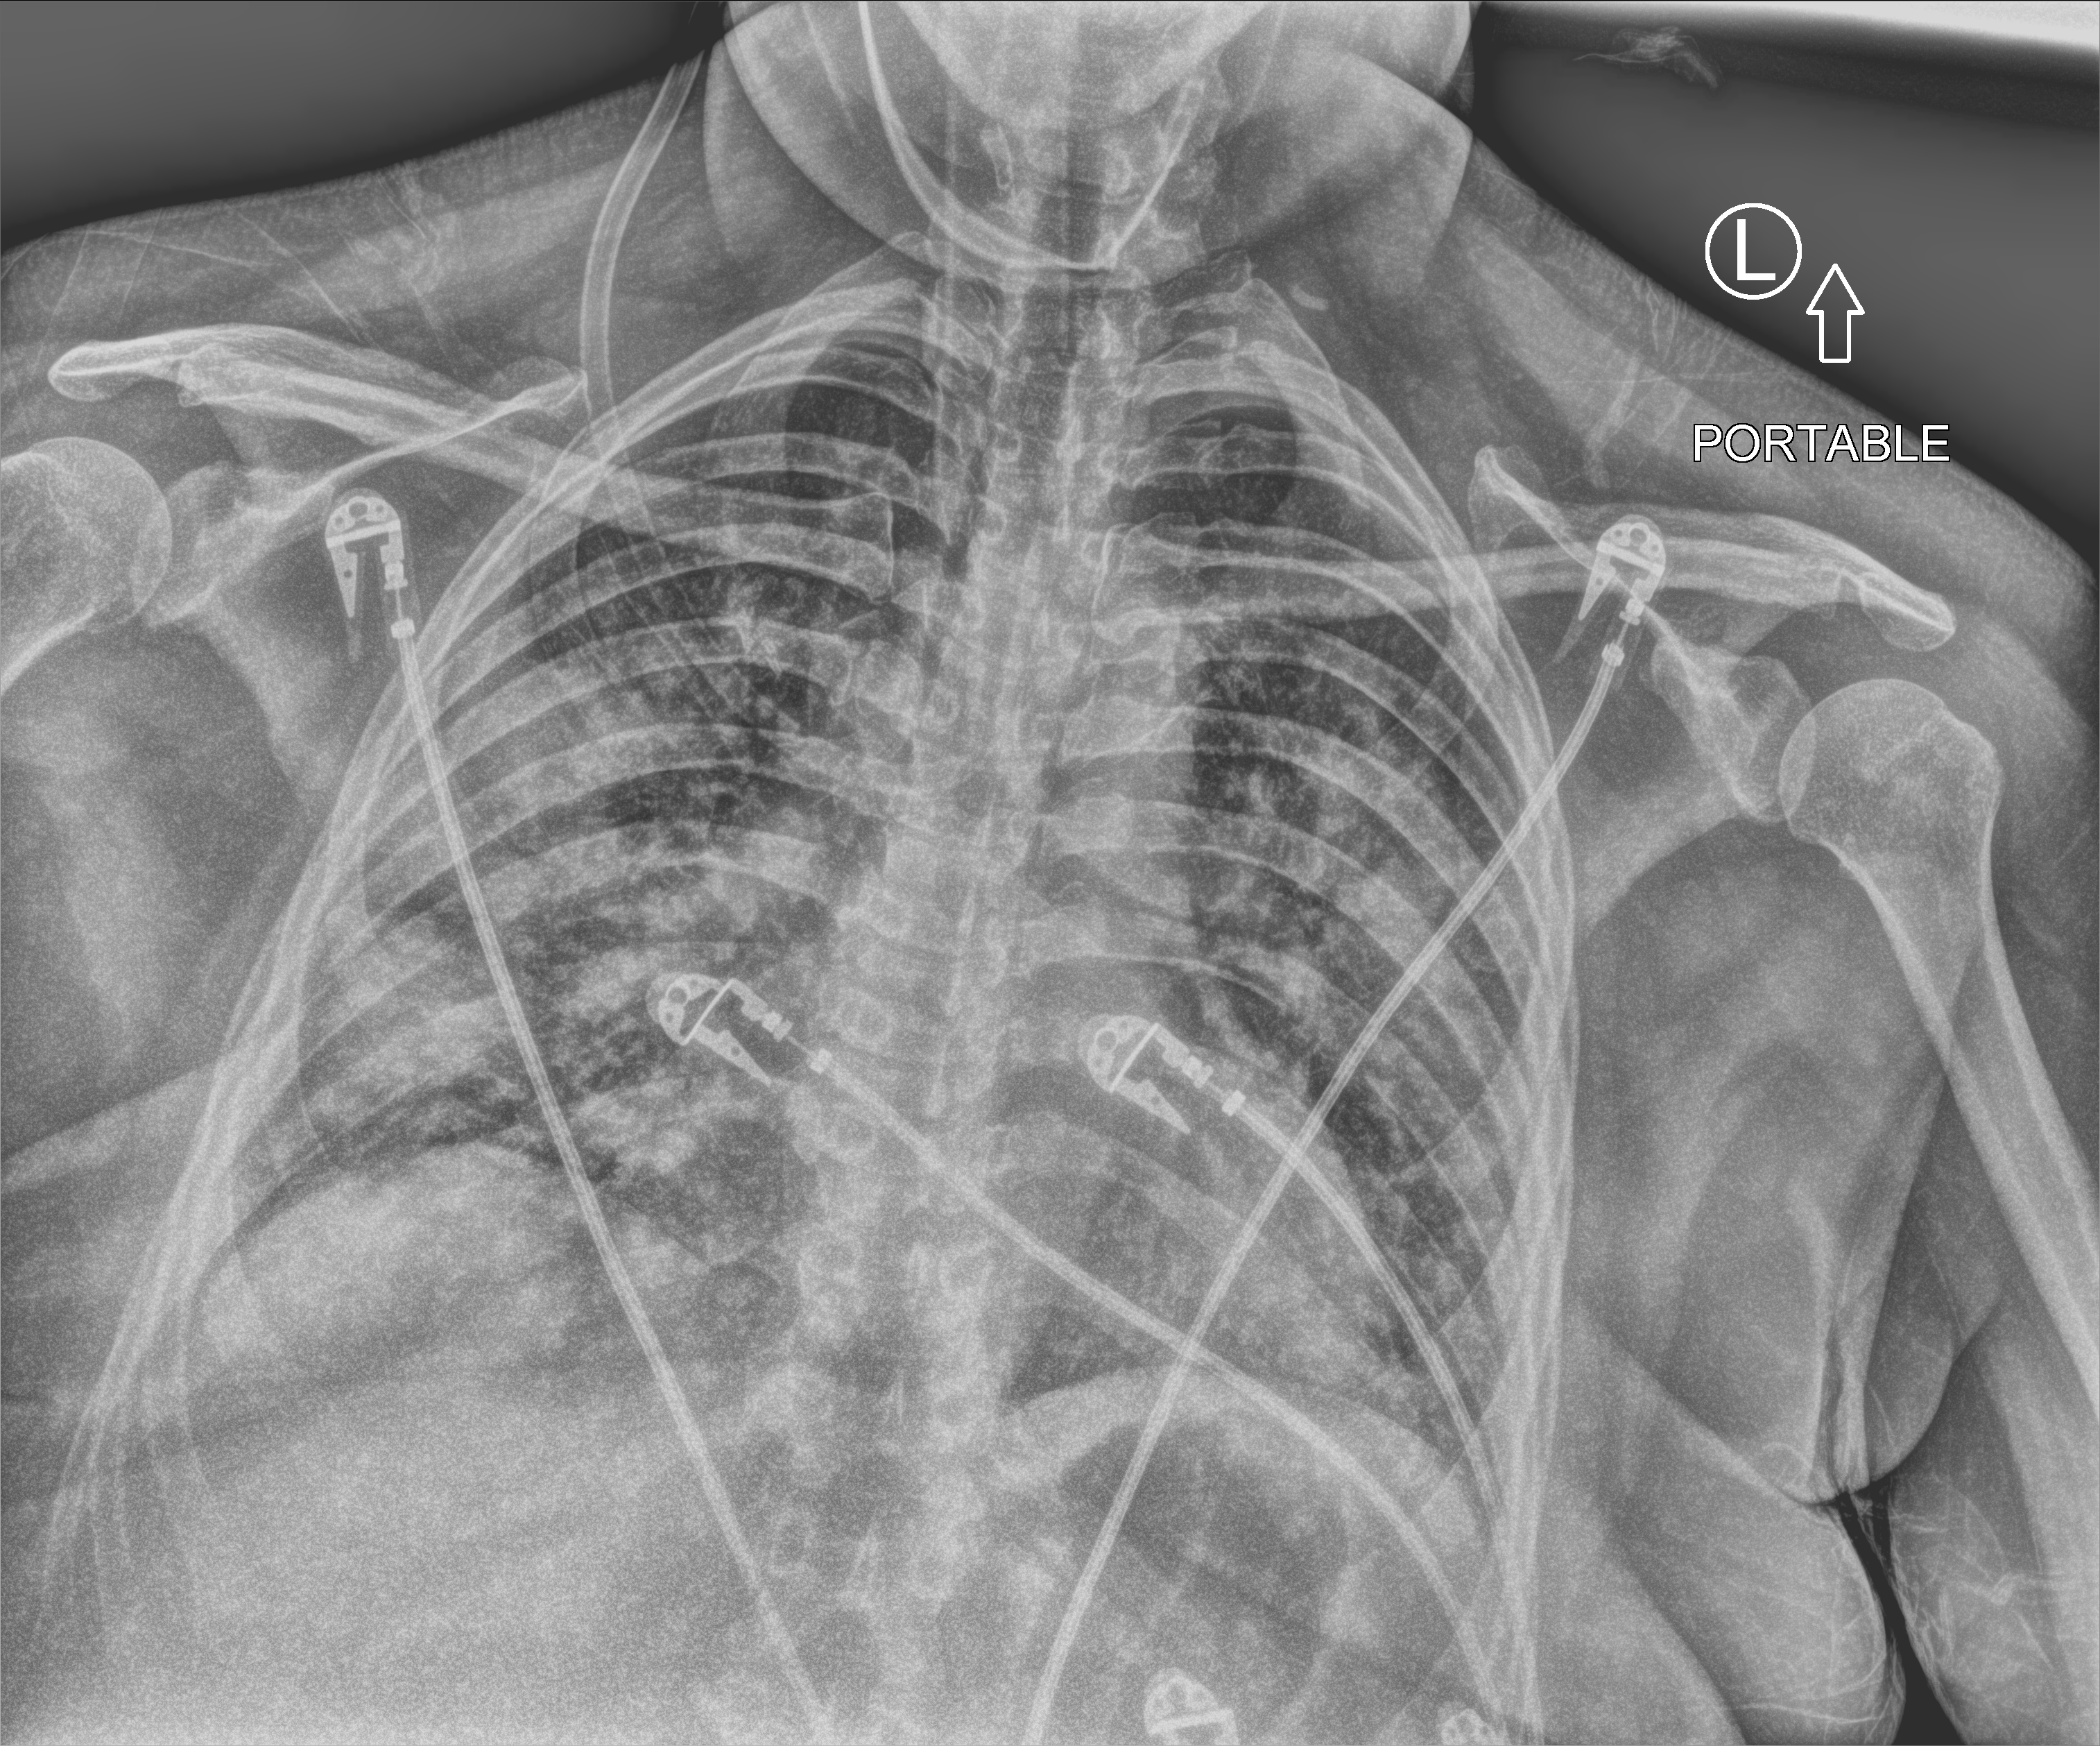
Bedside chest radiograph (computed radiography); anteroposterior (AP) projection. Female patient hospitalised with COVID-19, age 18–59 years.
From the hospital-stay record, not from the radiograph (when in the stay this image was taken is not recorded): mechanically ventilated during this hospital stay: no; diabetes (admission record): yes.